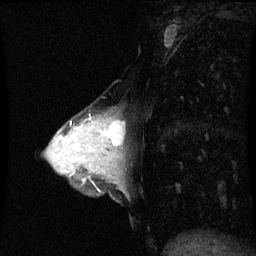
Breast MRI (dynamic contrast-enhanced), one sagittal slice; slice 28 of 60 in the series (ordered by position); dynamic contrast-enhanced series, image 2 of 3 at this slice position (ordered by acquisition); 1.5 T; TE 4.2 ms, TR 8.9 ms; 256 × 256 image matrix, field of view 200 × 200 mm. Female patient, age 33 years. Case-level facts recorded for this patient, not image findings: setting: breast cancer imaged before/during neoadjuvant chemotherapy; receptor status: HER2-positive.
Outlined on this slice (semi-automatically segmented with operator editing):
- analysis volume of interest (the breast-tissue region the enhancement analysis was run in; not a lesion): bounding box <95,116,125,153> (left, top, right, bottom; pixels)
- tumour enhancement mask (voxels above the 70 % enhancement threshold inside the analysis volume of interest): <107,120,123,145>